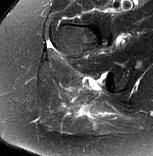
MRI of an extremity soft-tissue mass, one axial slice. Slice 55 of 77 in the series (ordered by position). T2-weighted fat-saturated. MR volume resampled by the dataset authors to the PET/CT grid (not the native acquisition matrix). 3.27 mm slice thickness. 153 × 156 image matrix, field of view 149 × 152 mm. Female patient. Case-level facts recorded for this patient, not image findings: histological type: synovial sarcoma; grade: intermediate; site of the primary tumour: right buttock.
Annotated regions visible in this slice (expert contour drawn on MRI and transferred to this co-registered scan by the dataset authors):
- gross tumour volume including surrounding oedema: bounding box [x1, y1, x2, y2] px = [67, 97, 98, 117]